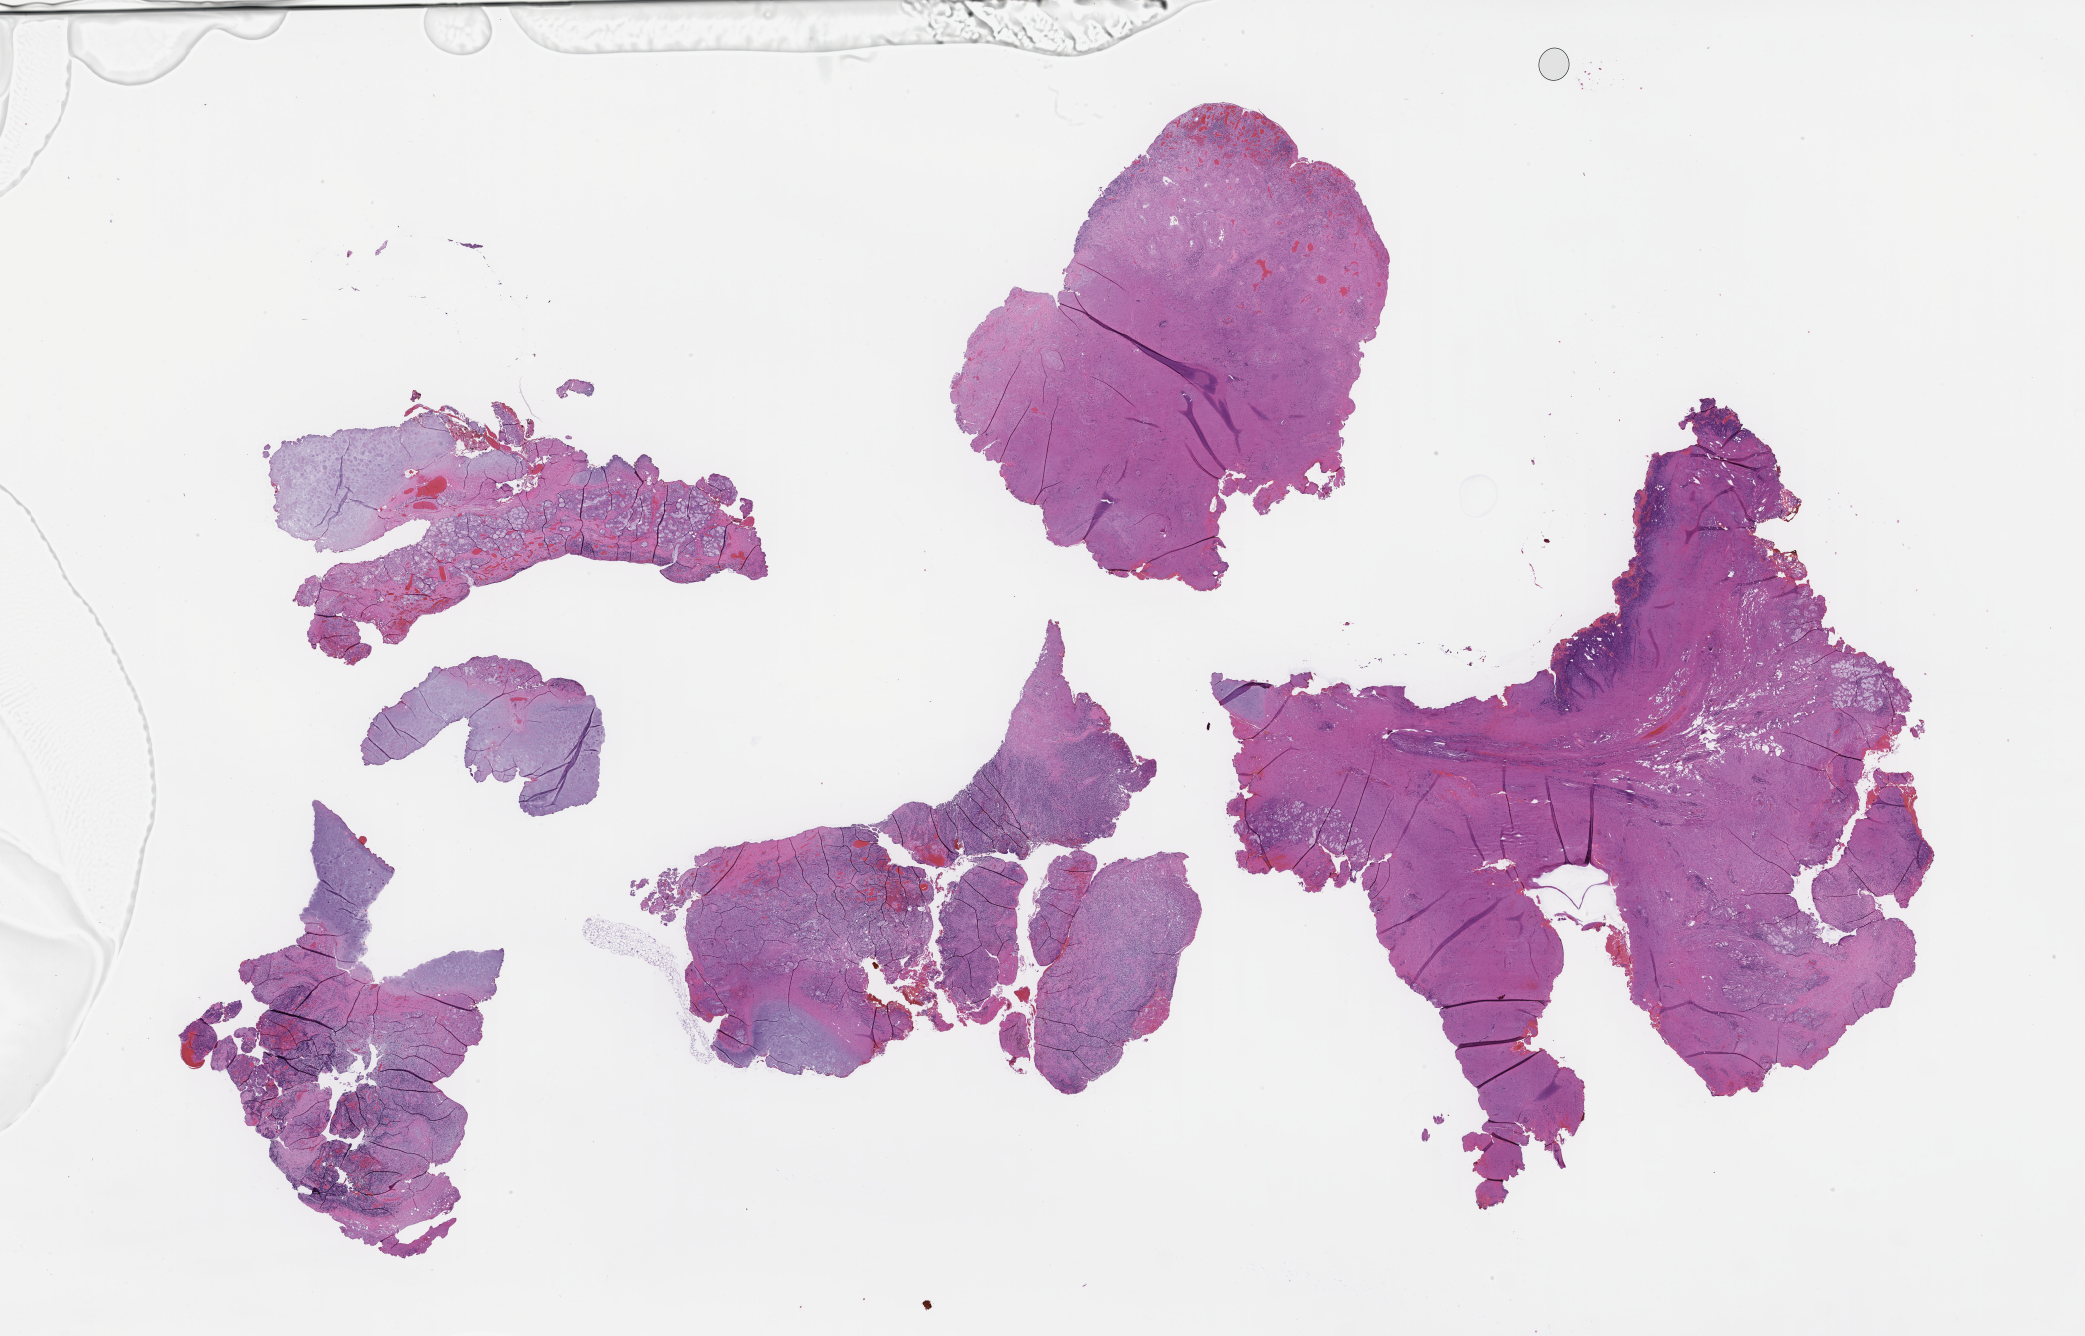
Whole-slide image, hematoxylin and eosin (H&E) stain — low-resolution overview of the scanned area, about 33.7 x 21.6 mm, formalin-fixed, paraffin-embedded (FFPE) tissue, site: skin, archival tissue. Patient sex: male.
* this section: primary tumor
* diagnosis: Melanoma